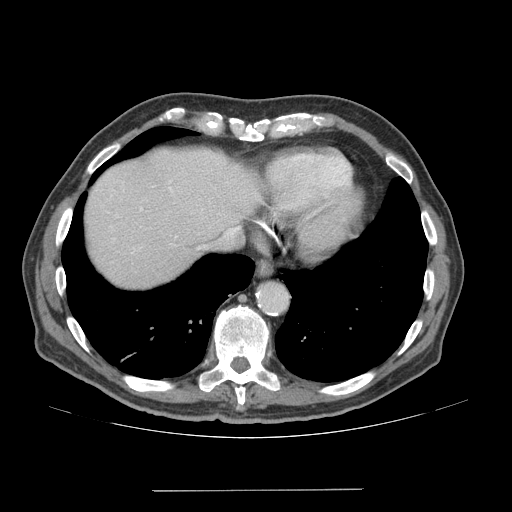
Contrast-enhanced abdominal CT (liver protocol), one axial slice; reconstruction kernel STANDARD; 140 kVp; soft-tissue window (W 400 / L 40 HU); 512 × 512 image matrix, field of view 400 × 400 mm. Case-level facts recorded for this patient, not image findings: diagnosis: hepatocellular carcinoma (patient treated with transarterial chemoembolisation; whether this scan precedes or follows treatment is not stated here); TNM stage (as recorded): Stage-IVA; Child-Pugh class: A; tumour differentiation: well differentiated.
Annotated regions visible in this slice (semi-automatic segmentation, software-assisted and operator-edited):
- abdominal aorta: bounding box (x1, y1, x2, y2) in pixels: (258, 284, 287, 312)
- liver parenchyma outside the tumour (the mass and vessels are separate outlines, so this box may not span the whole liver): (86, 148, 260, 288)
- liver vessels: (140, 187, 172, 211)